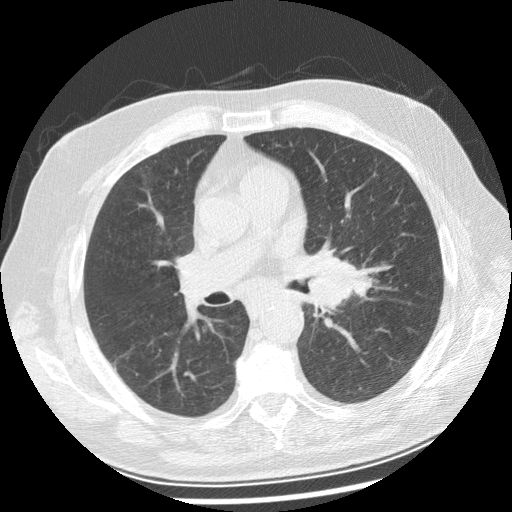
Low-dose screening chest CT, axial slice, baseline annual screen, lung window (W 1500 / L -600 HU), 2.5 mm slice thickness, standard (soft-tissue) reconstruction kernel (STANDARD), slice 110 of 250 in the series, 512 × 512 image matrix. Male, age 70 years at enrolment. Current smoker at enrolment.
Expert-annotated lung lesion, bounding box (x1, y1, x2, y2) in pixels: (285, 241, 367, 314). No non-calcified nodule or mass ≥4 mm was recorded by the screening reader at this exam.